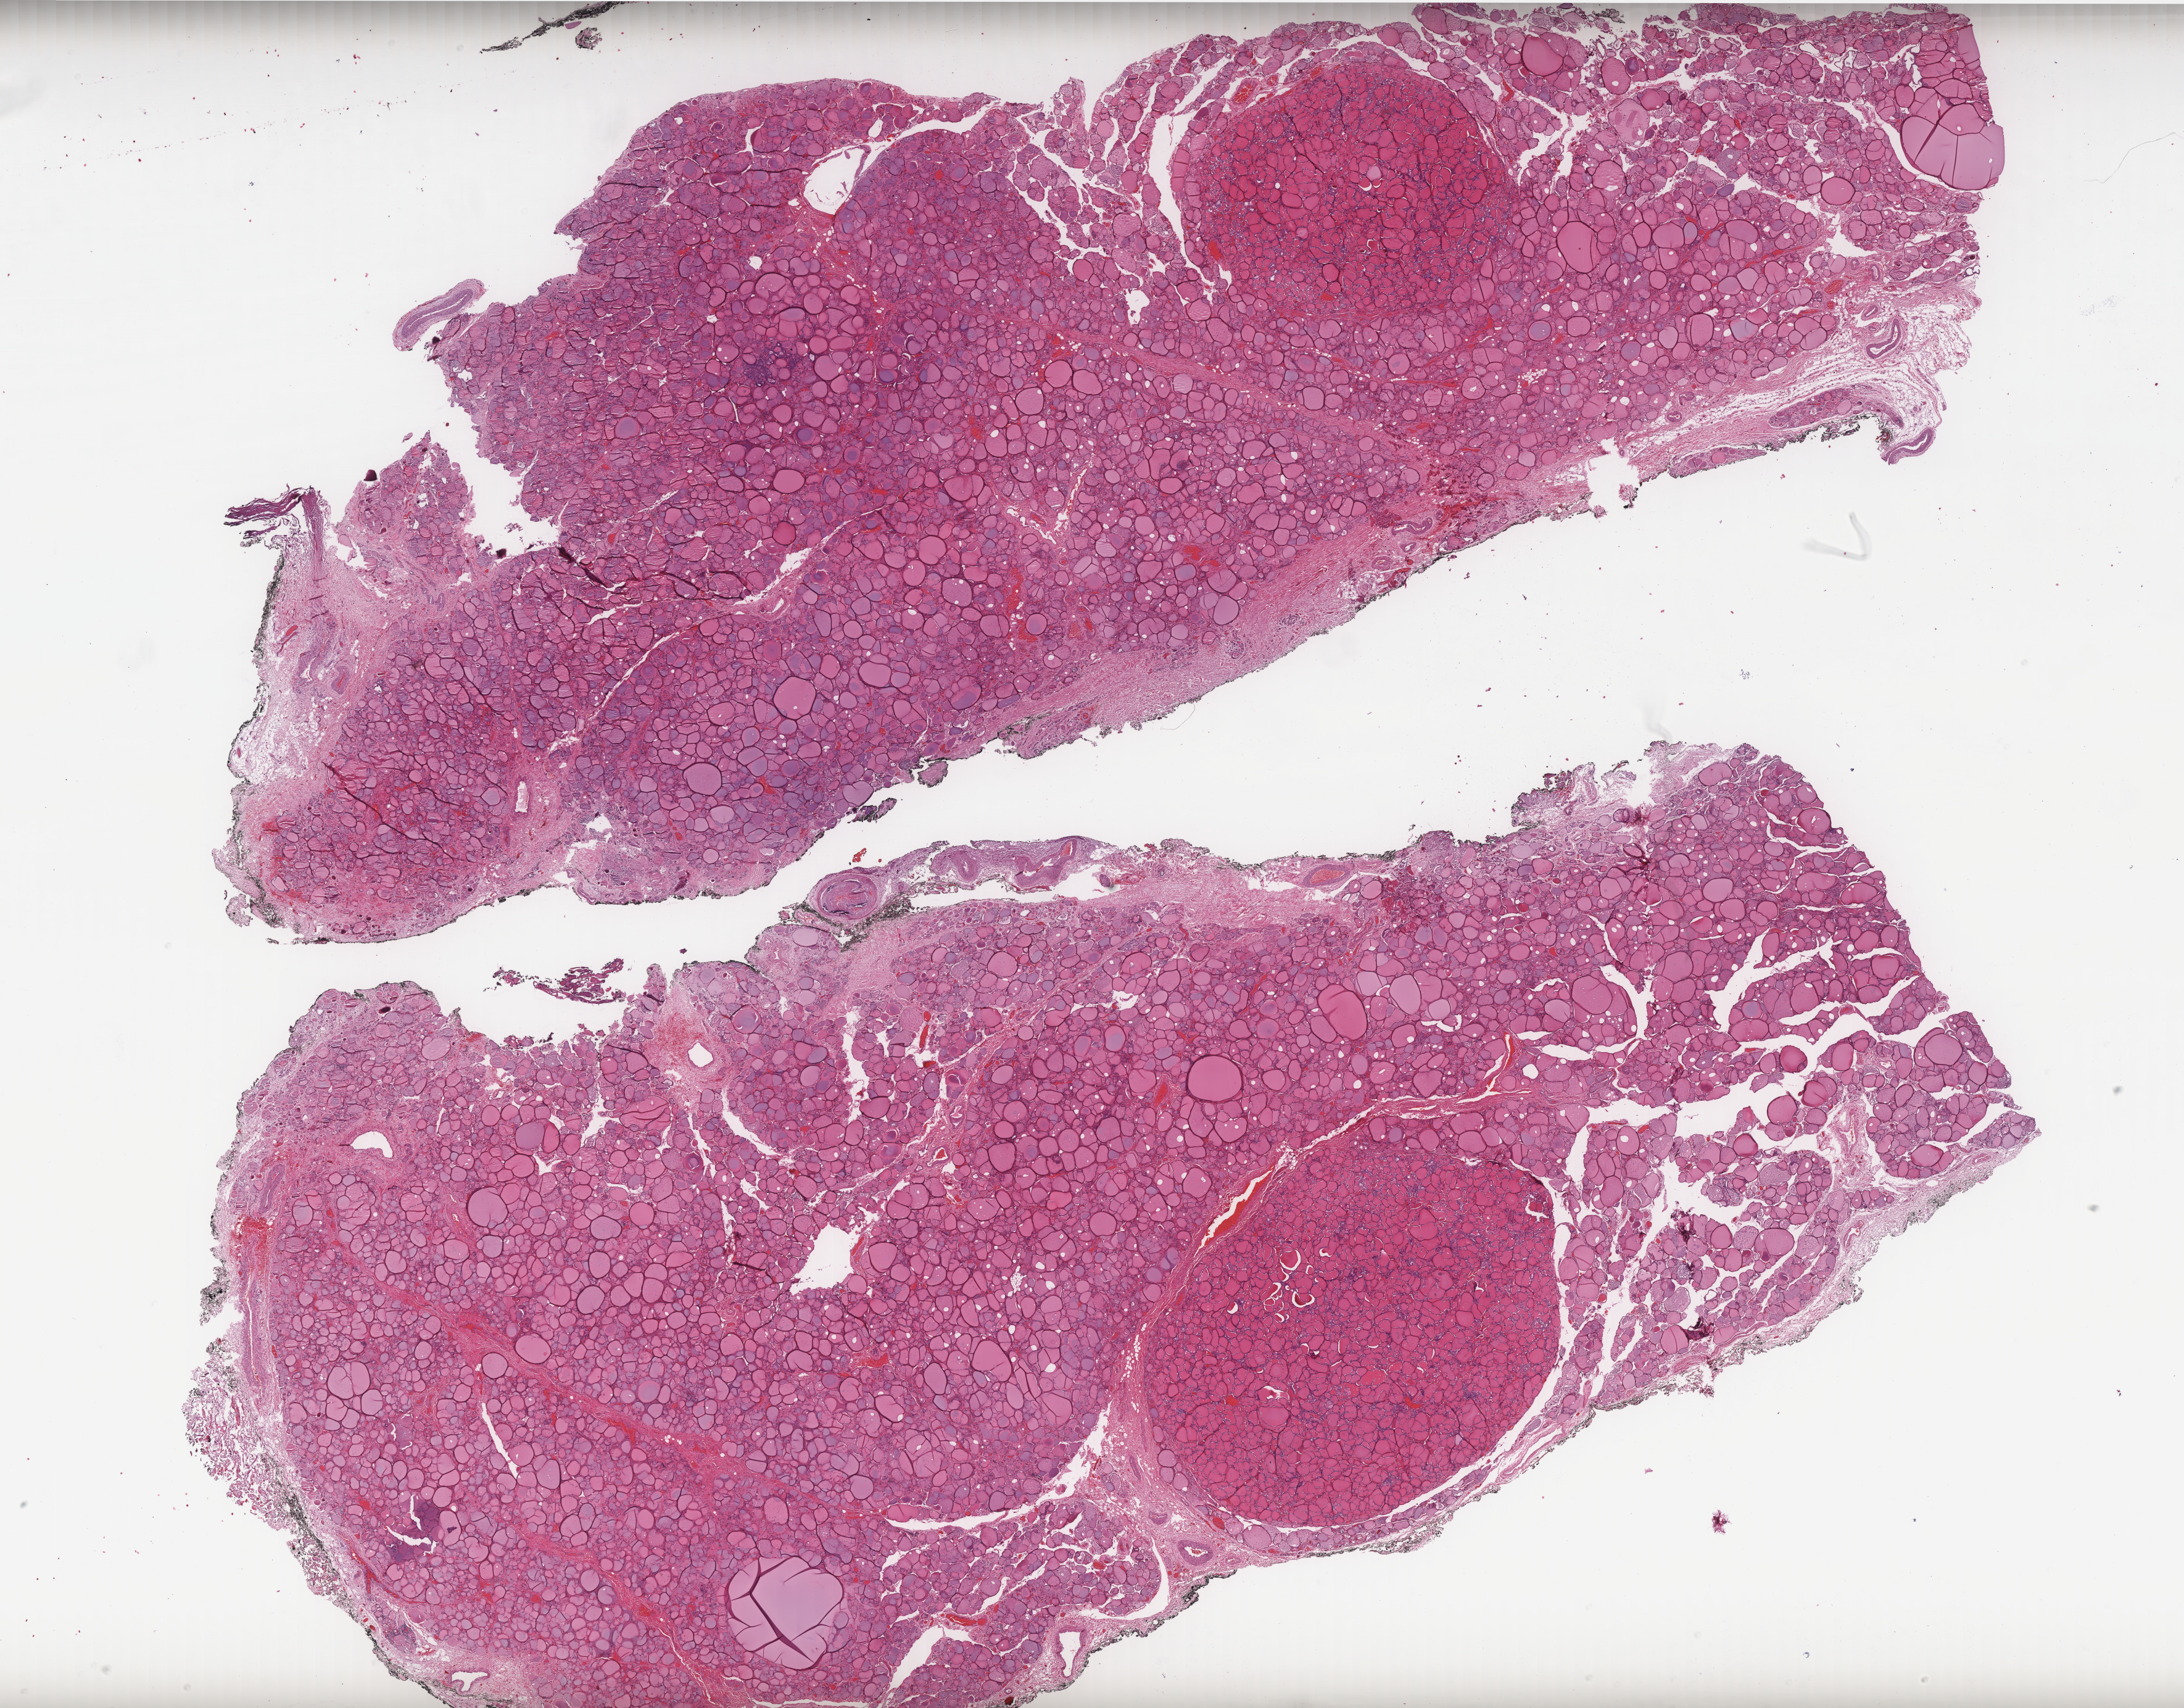
Whole-slide histology image, H&E — low-resolution overview of the scanned area, about 28.4 x 22.2 mm; FFPE section; thyroid, primary tumour sample. Patient: male, age at initial diagnosis 80 years.
Histologic diagnosis: Papillary carcinoma, follicular variant (thyroid gland). Laterality: bilateral. AJCC pathologic stage: I (7th edition).